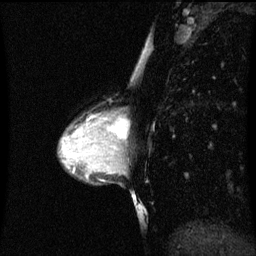
Breast MRI (dynamic contrast-enhanced), one sagittal slice; slice 32 of 60 in the series (ordered by position); dynamic contrast-enhanced series, image 2 of 3 at this slice position (ordered by acquisition); 1.5 T; TE 4.2 ms, TR 8.9 ms; 2 mm slice thickness; 256 × 256 image matrix, field of view 200 × 200 mm. Patient: female, 33 years. Case-level facts recorded for this patient, not image findings: setting: breast cancer imaged before/during neoadjuvant chemotherapy; receptor status: HER2-positive.
Outlined on this slice (semi-automatic segmentation, software-assisted and operator-edited):
- analysis volume of interest (the breast-tissue region the enhancement analysis was run in; not a lesion): bounding box <107,108,123,147> (left, top, right, bottom; pixels)
- tumour enhancement mask (voxels above the 70 % enhancement threshold inside the analysis volume of interest): <109,118,122,141>